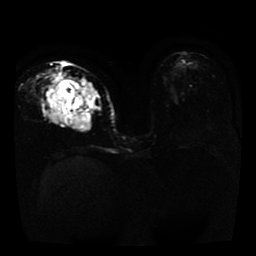
Breast MRI, one axial slice; position 18 of 41 along the scan axis; diffusion-weighted series; image 2 of 4 stored at this slice position (different b-values; order by instance number); 1.5 T; 256 × 256 image matrix, field of view 330 × 330 mm. Female patient.
Outlined on this slice (expert manual segmentation):
- tumour on diffusion-weighted imaging: bounding box [x1, y1, x2, y2] px = [47, 74, 96, 128]